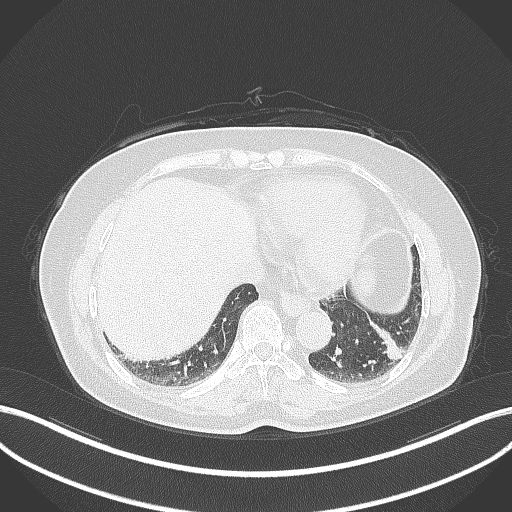
Chest CT, one axial slice. Slice 106 of 311 in the series (ordered by position). 120 kVp. Lung window (W 1500 / L -600 HU). 1 mm slice thickness. 512 × 512 image matrix, field of view 400 × 400 mm. Patient: female, 59 years. From the clinical record (not read from this slice): clinical TNM (as recorded): T2a N0 M0; histopathological grade: G2-3.
Structures marked on this image (rectangle marked by the reading radiologist):
- lung tumour (recorded histology: adenocarcinoma): bounding box <368,319,408,365> (left, top, right, bottom; pixels)